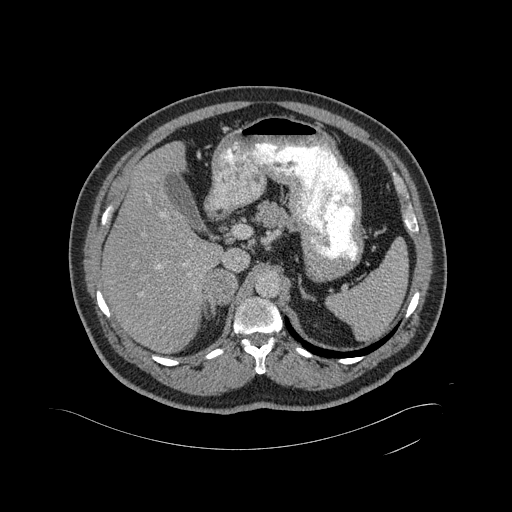
Contrast-enhanced abdominal CT, one axial slice. Slice 323 of 433 in the series (ordered by position). 120 kVp. Intravenous contrast given. Soft-tissue window (W 400 / L 40 HU). 2 mm slice thickness. 512 × 512 image matrix. Patient: male, 56 years. From the clinical record (not read from this slice): diagnosis: adrenocortical carcinoma; tumour side: right adrenal; tumour size at pathology: 11.6 cm; Ki-67 index: 50 %; stage (as recorded): 3.
Structures marked on this image (semi-automatically segmented with operator editing):
- mass: box from (x=205, y=270) to (x=236, y=304) px